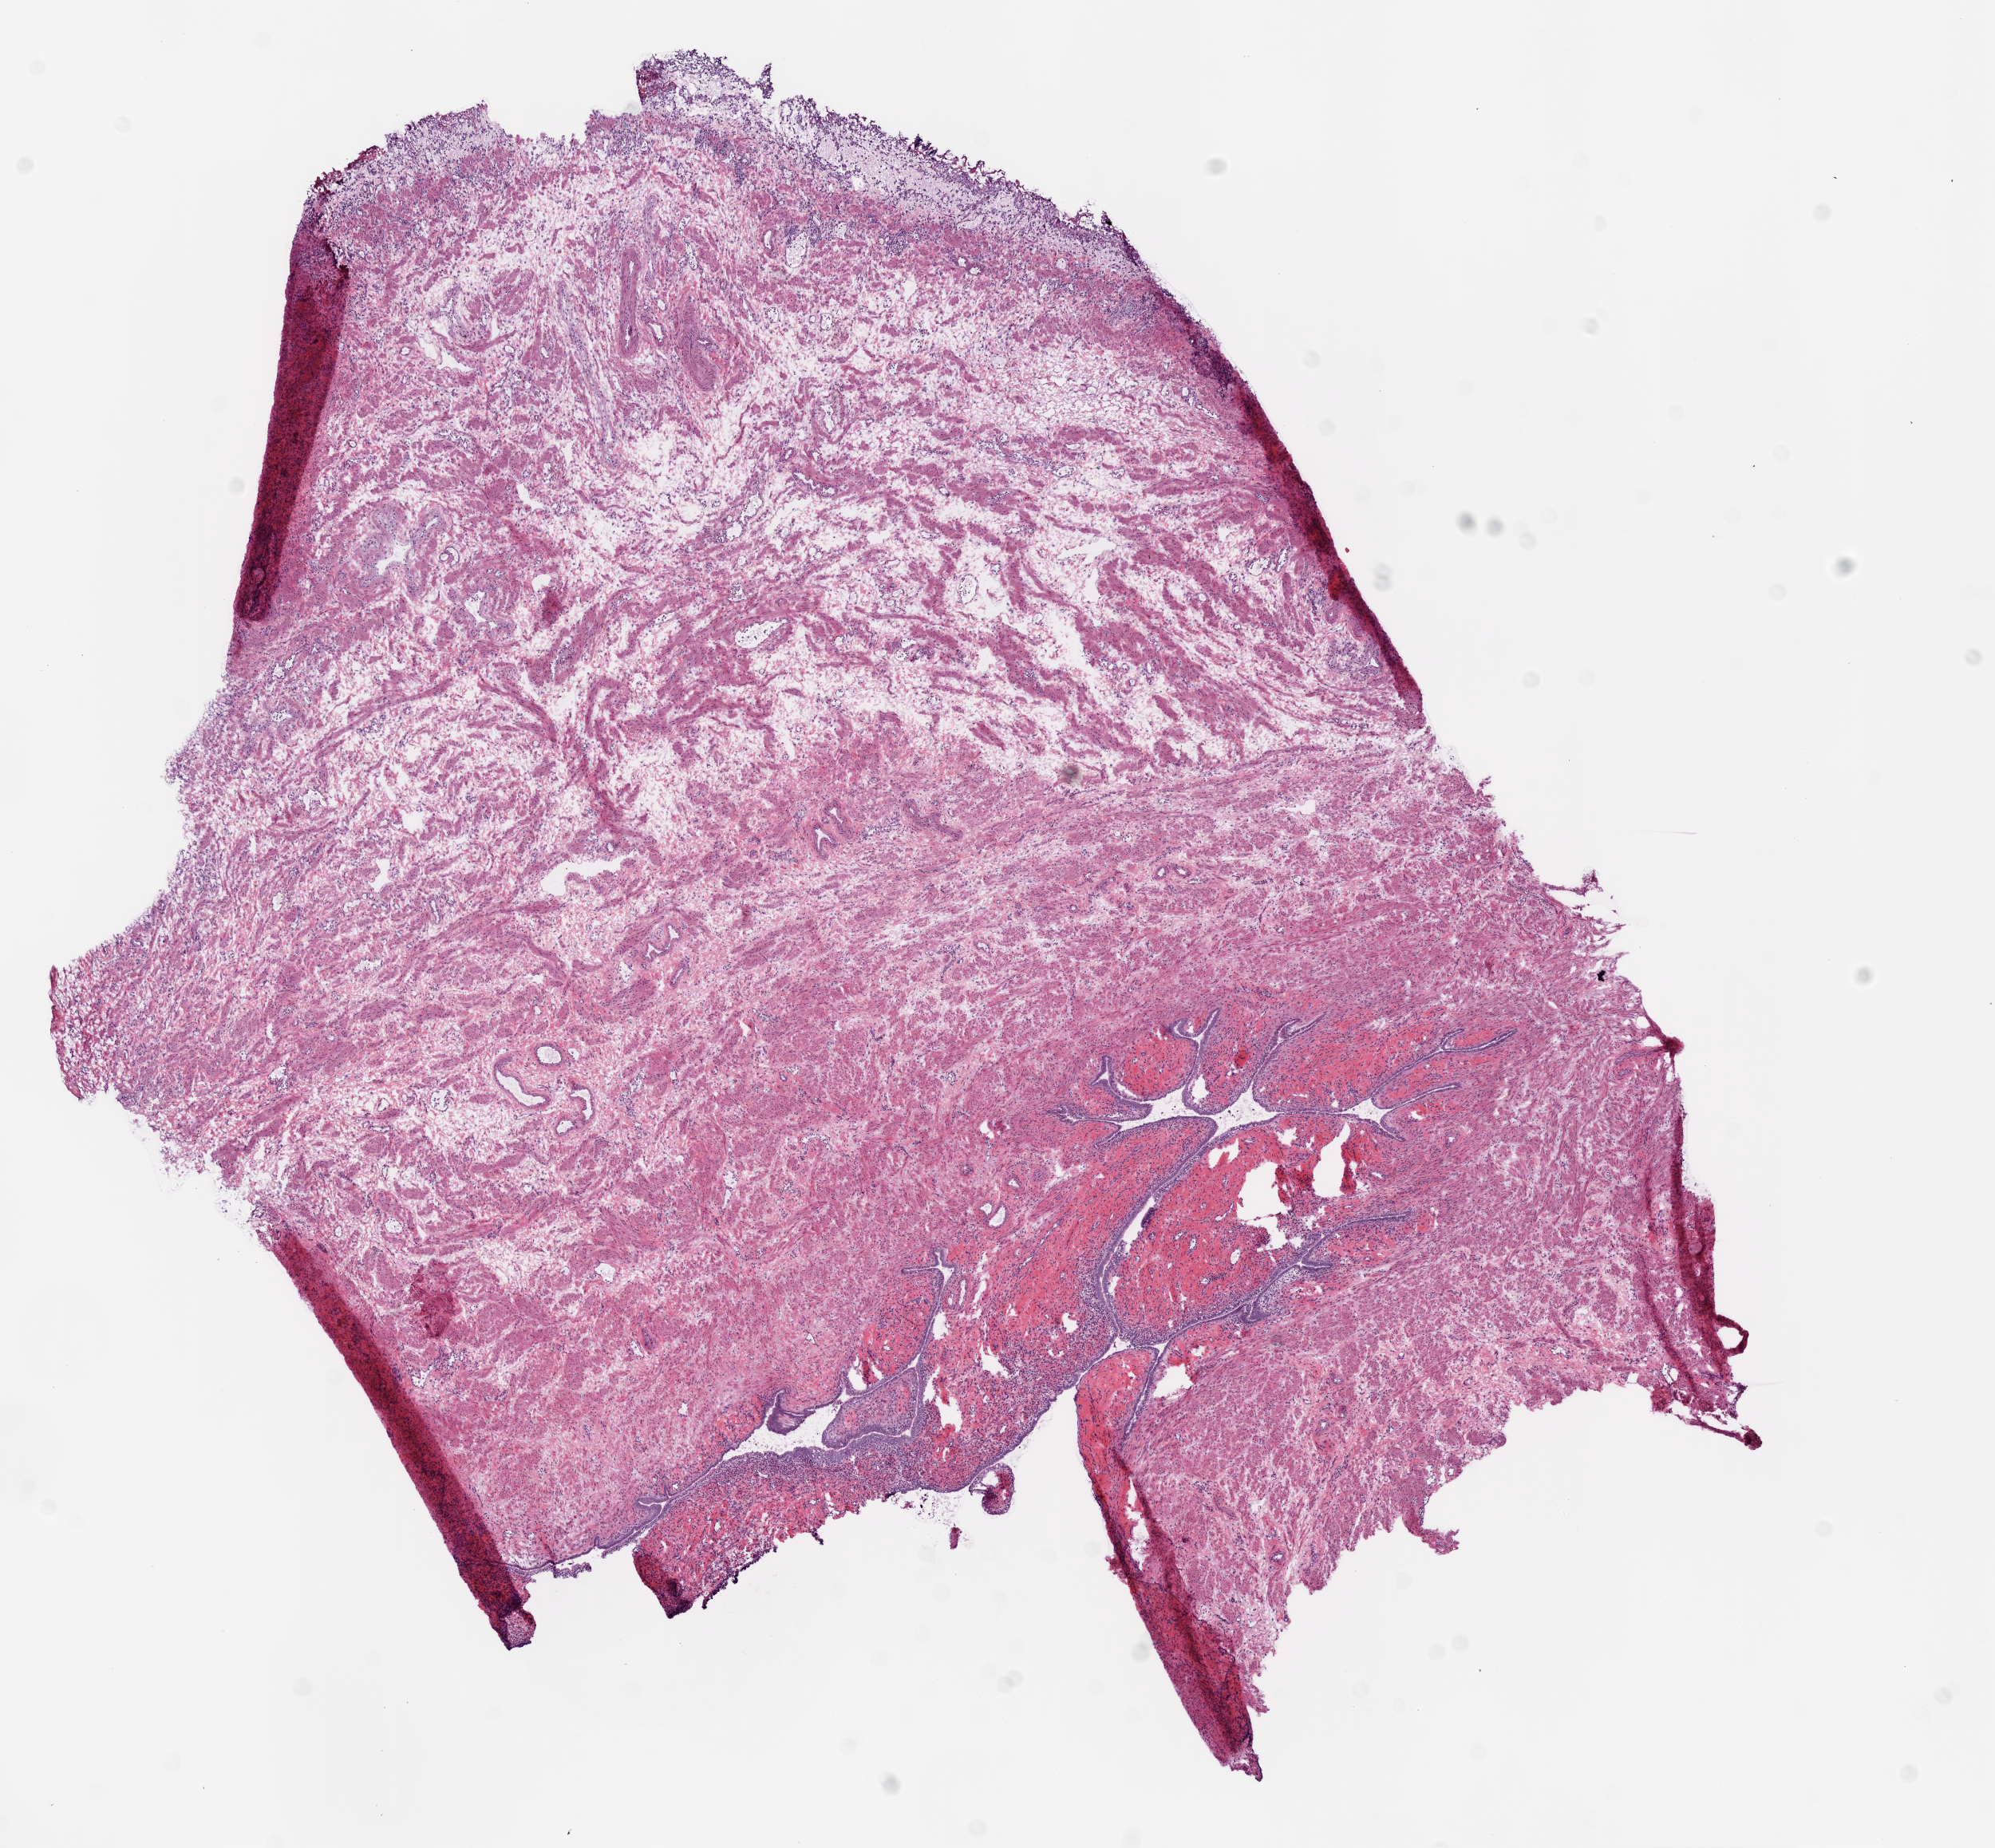
H&E whole-slide image — whole scanned area (about 10.0 x 9.3 mm, slide scanned at 20x) shown as a low-resolution overview. Frozen section from the bottom of the tissue portion. Ovary, solid tissue normal (non-tumour tissue) sample. Female, age 58 years at initial diagnosis.
This section: solid tissue normal sample (biorepository sample class). Patient diagnosis: Serous cystadenocarcinoma, NOS.